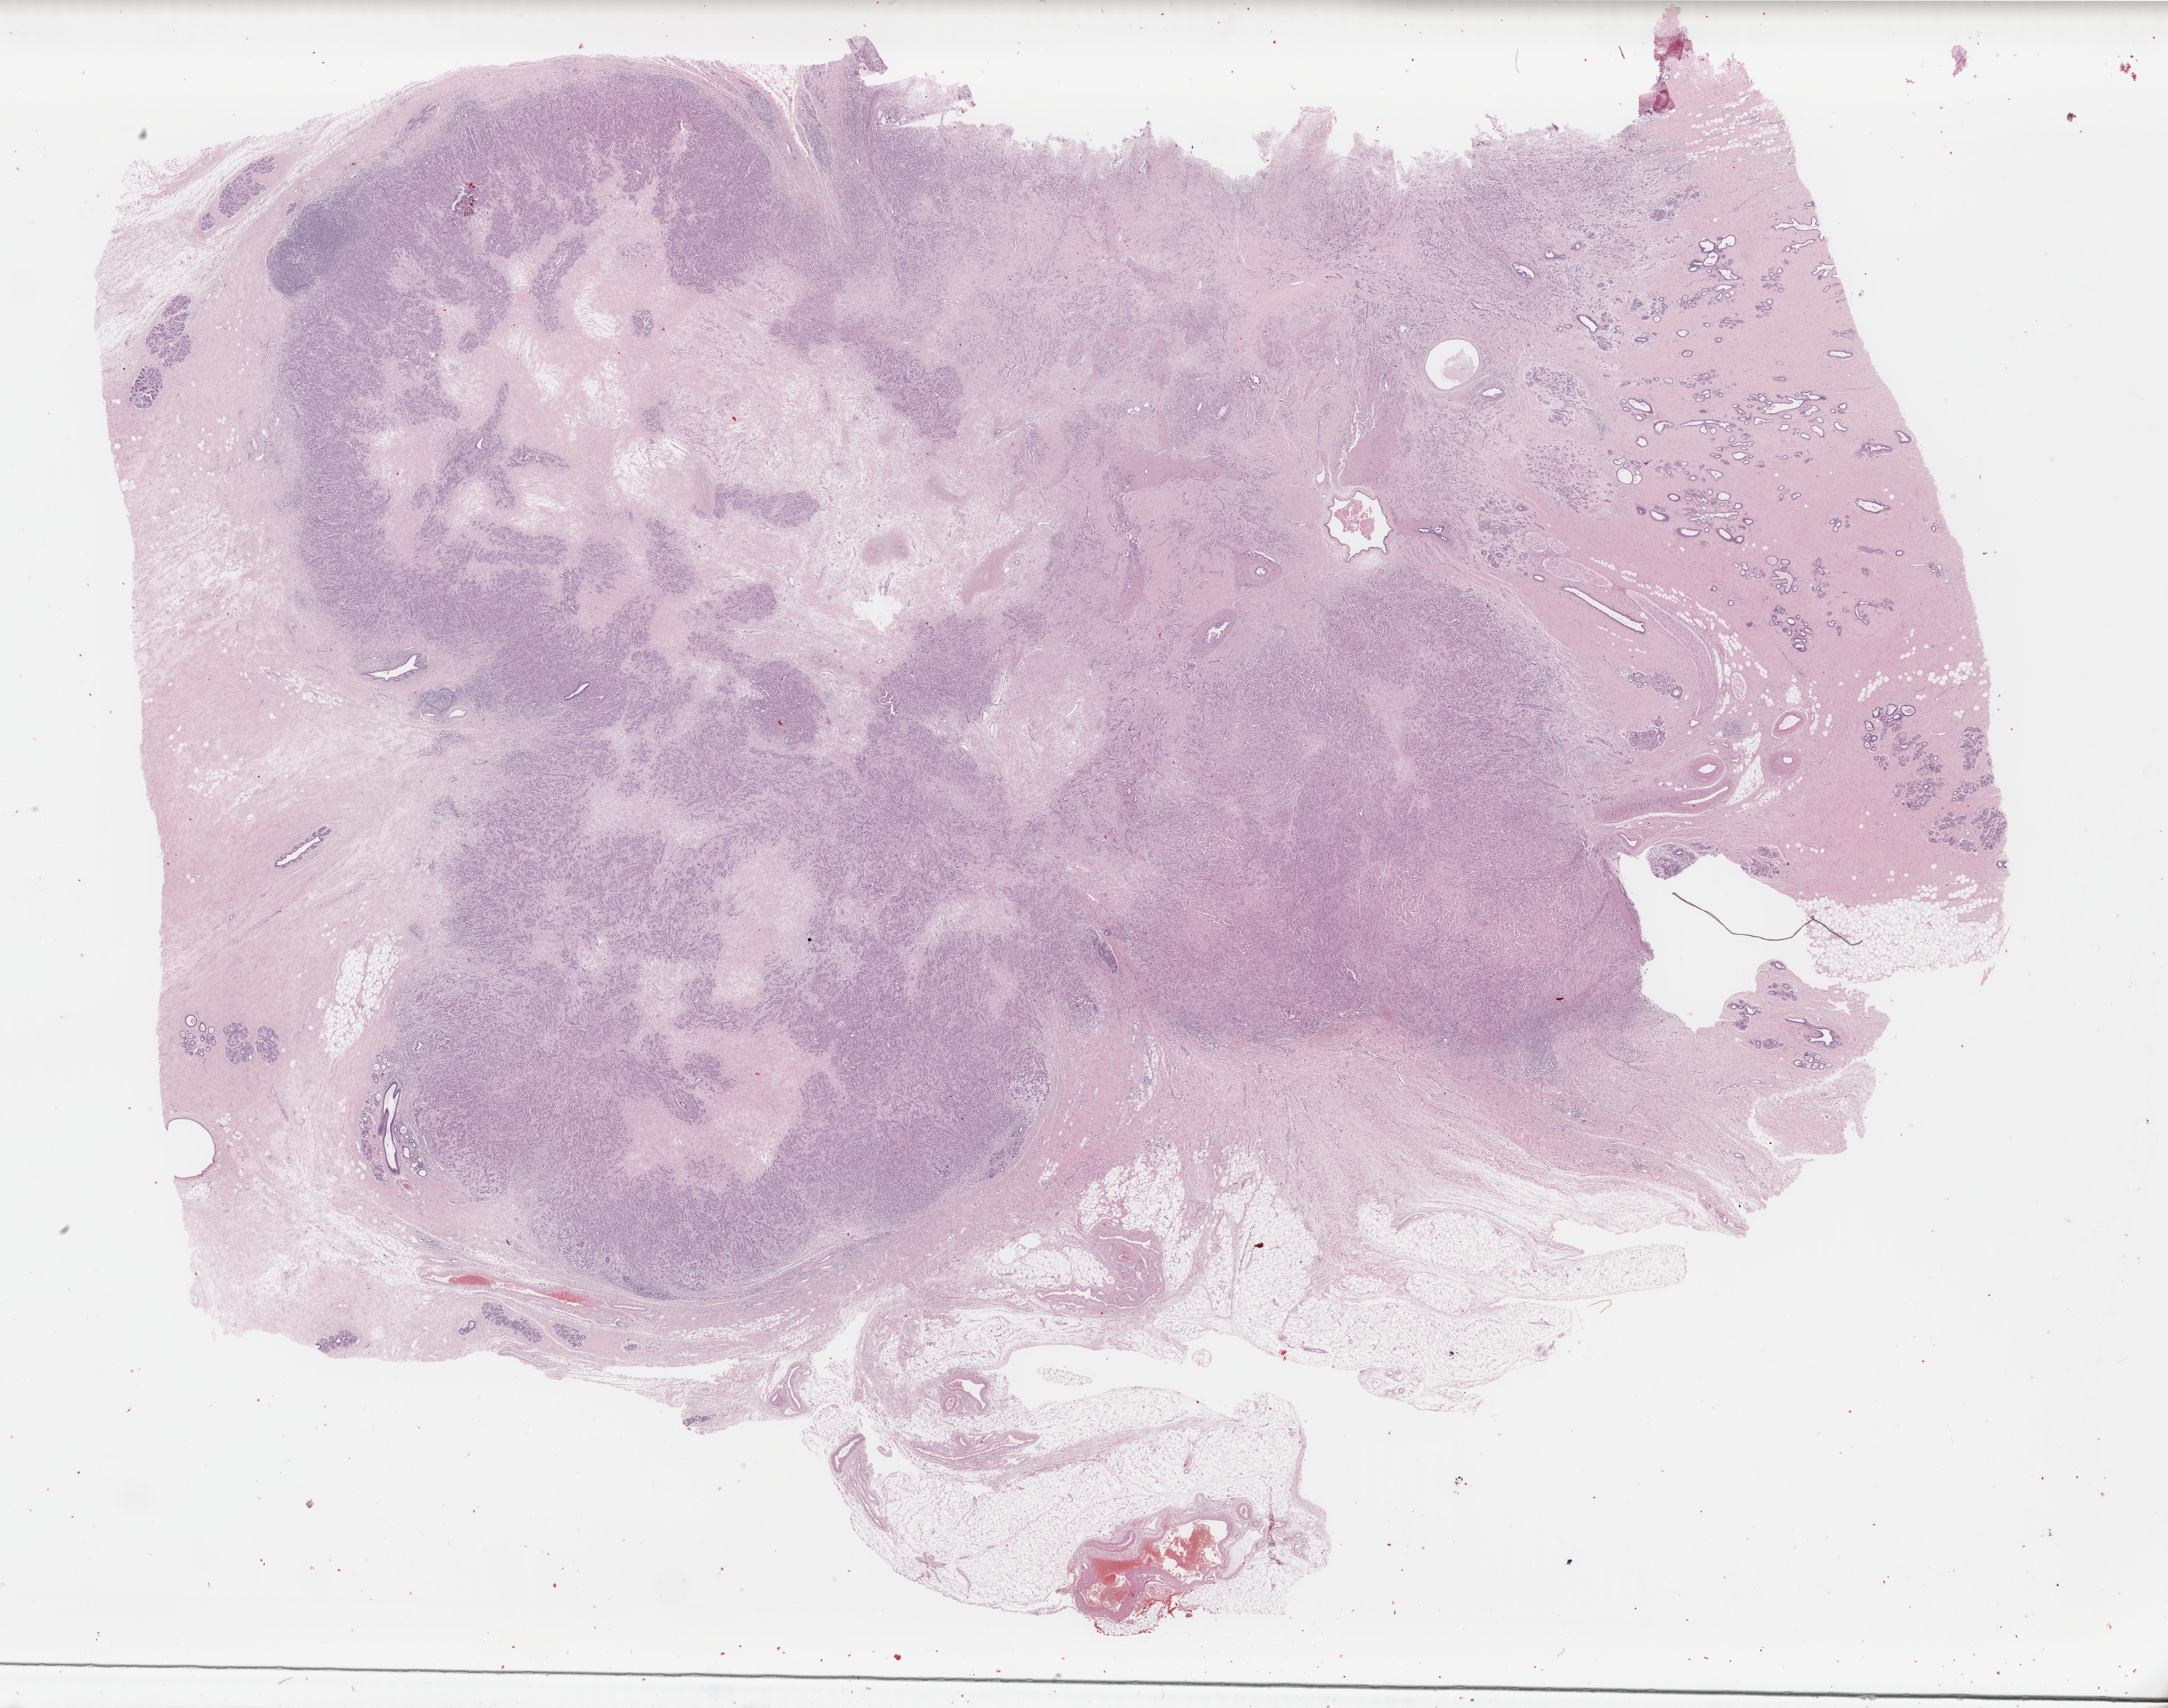
Whole-slide histology image, H&E-stained, whole scanned area (about 30.2 x 23.8 mm, acquisition: 40x scan) shown as a low-resolution overview; FFPE section; primary tumour sample from the breast. Female, age 48 years at initial diagnosis.
Laterality: left. AJCC pathologic stage: IA (7th edition). Histologic diagnosis: Infiltrating duct carcinoma, NOS.